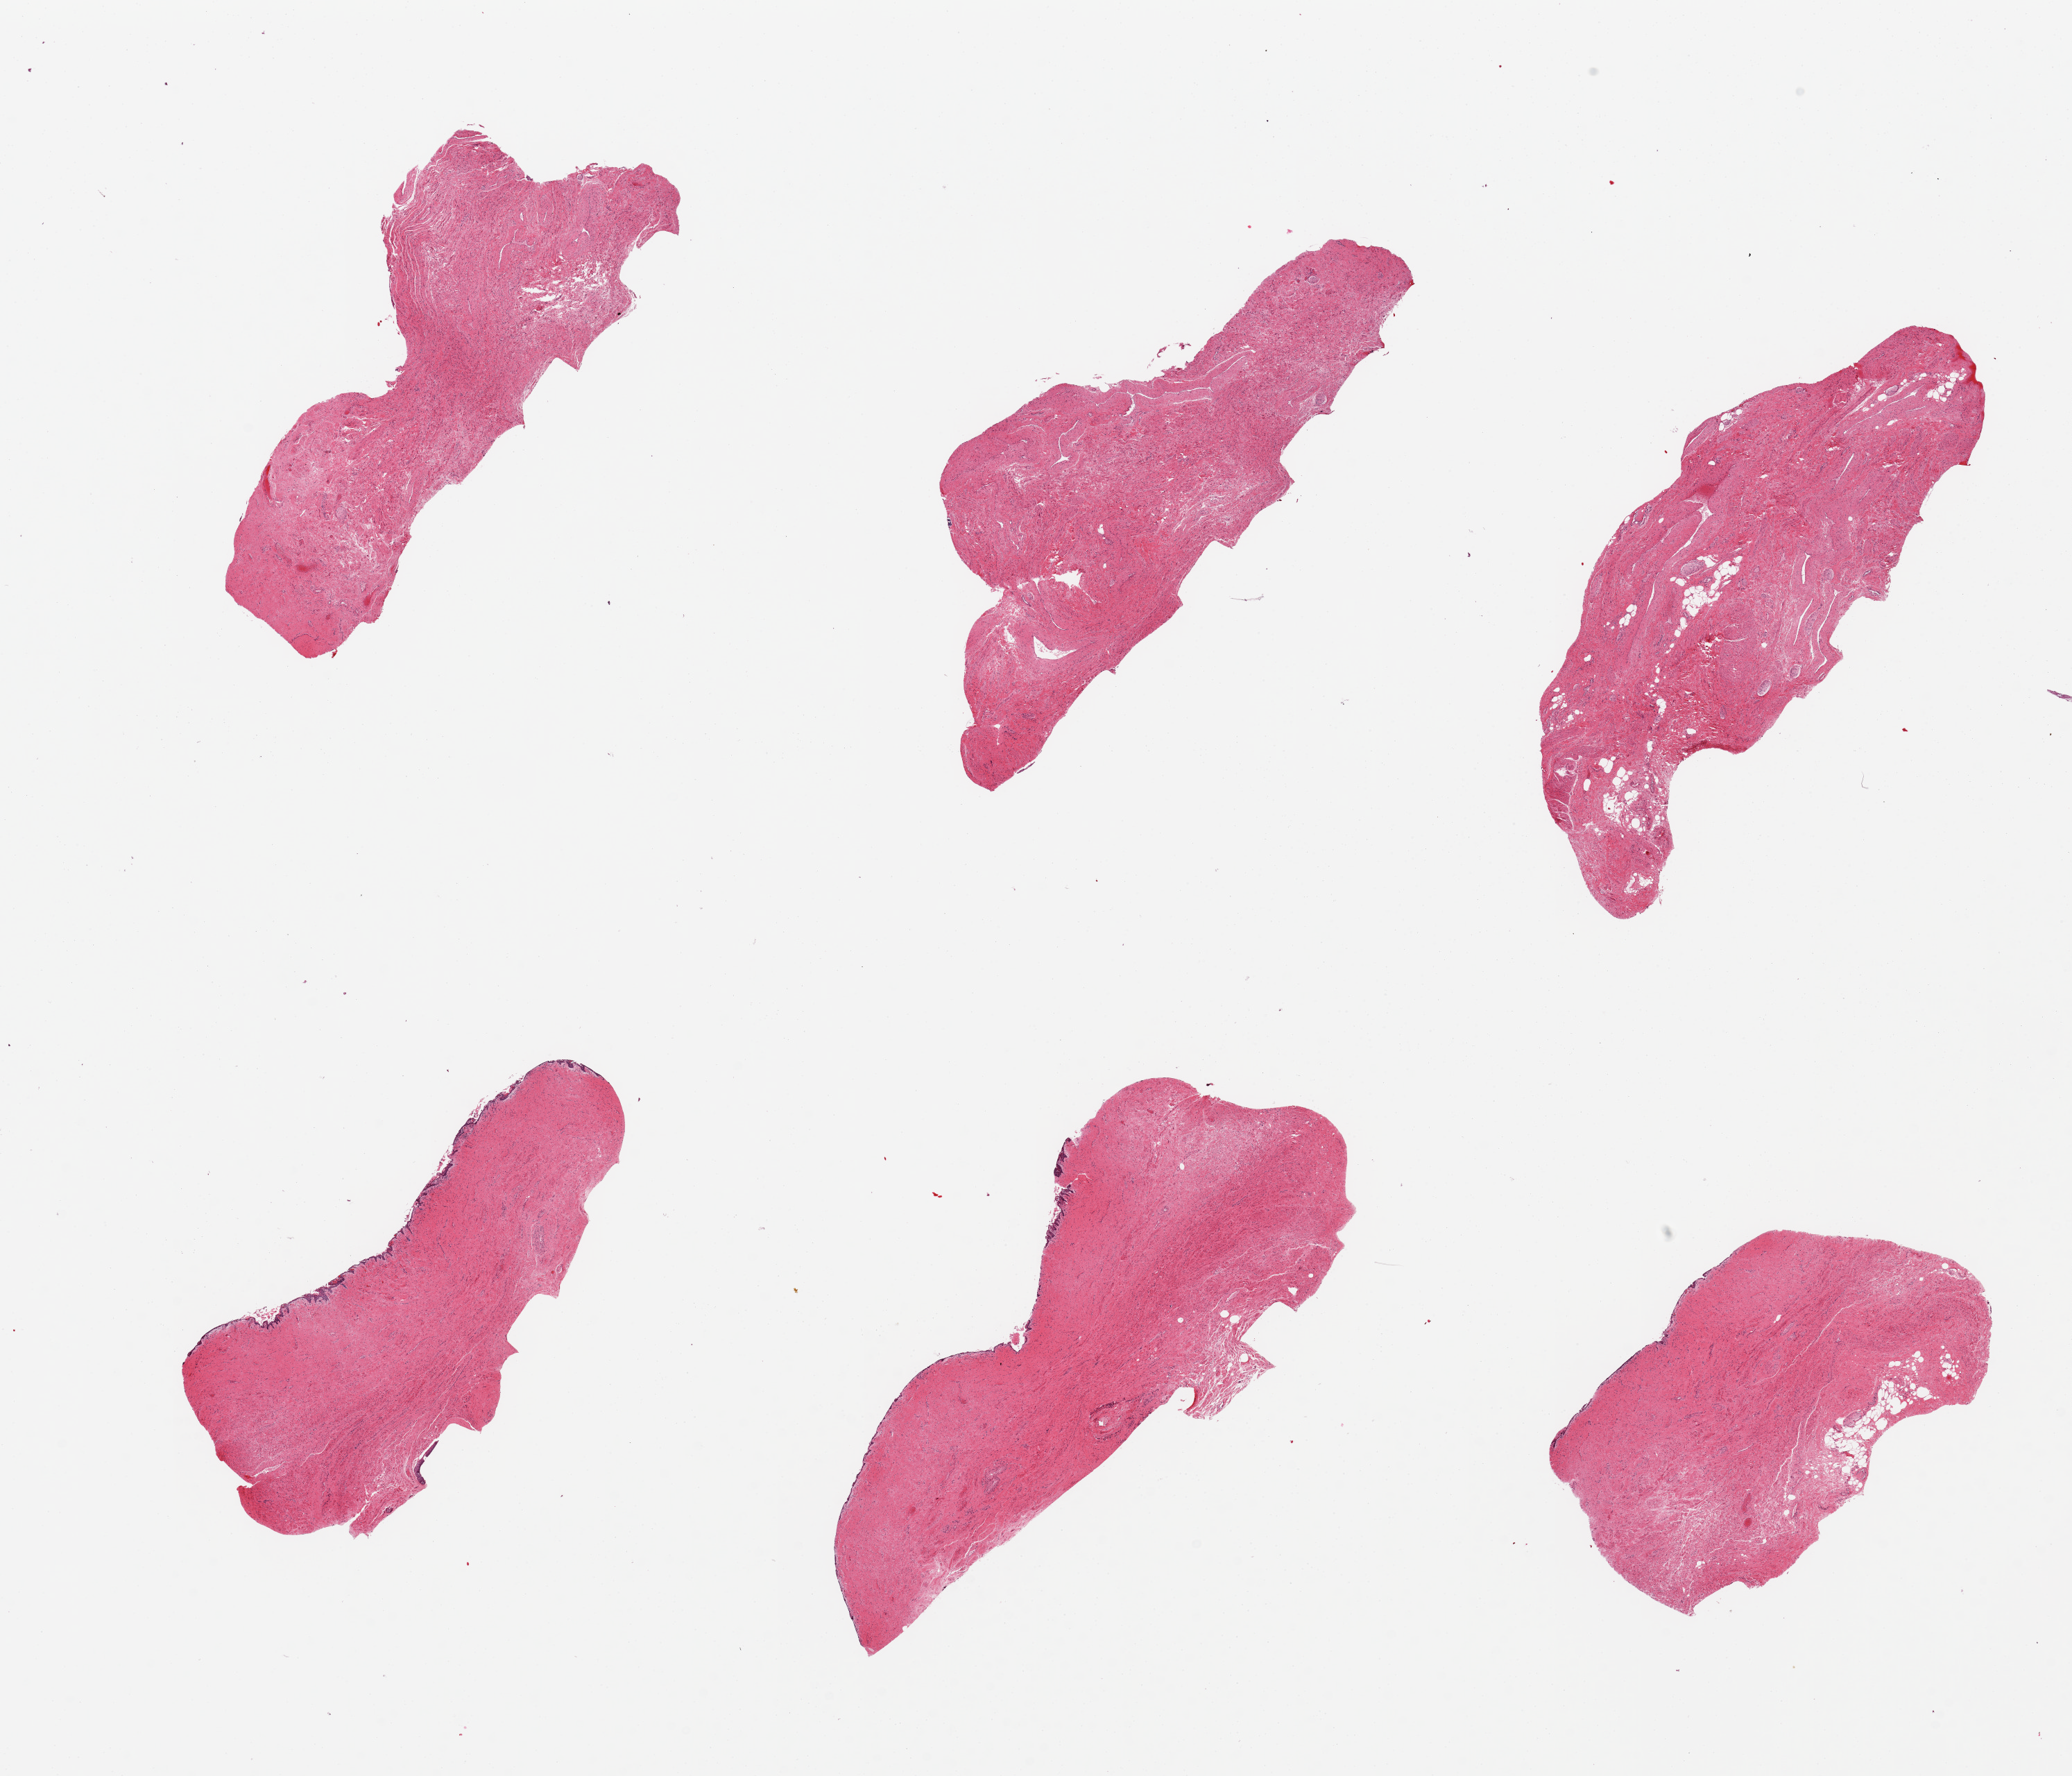
H&E whole-slide image — low-resolution overview of the scanned area, about 23.6 x 20.2 mm. PAXgene-fixed paraffin-embedded (PFPE) section. Sampled site (target tissue): vagina. Tissue donor sample. Female donor.
Reviewer comment on this tissue sample: 6 pieces, markedly autolyzed, squamous mucosa sloughed.